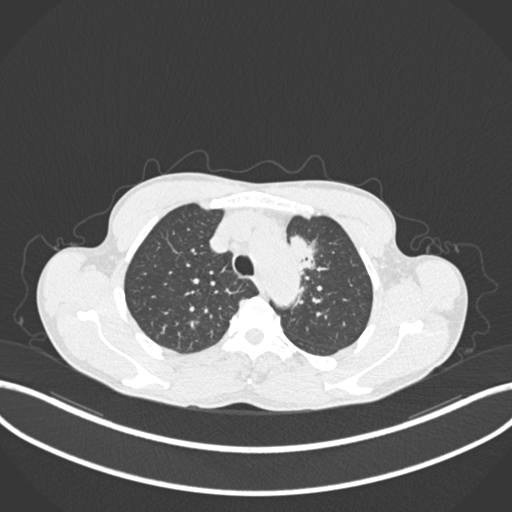
Chest CT, one axial slice; slice 159 of 211 in the series (ordered by position); 120 kVp; lung window (W 1500 / L -600 HU); 1 mm slice thickness; 512 × 512 image matrix, field of view 400 × 400 mm. Male patient, age 58 years. Case-level facts recorded for this patient, not image findings: clinical TNM (as recorded): T1c N1 M0.
Outlined on this slice (bounding box drawn by a radiologist):
- lung tumour (recorded histology: adenocarcinoma): bounding box (x1, y1, x2, y2) in pixels: (284, 228, 322, 277)